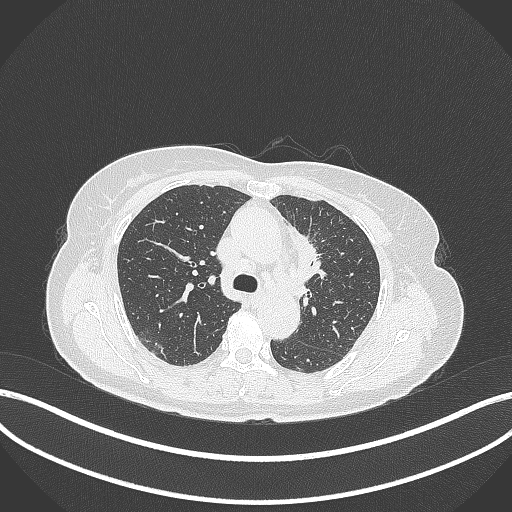
Chest CT, one axial slice. Slice 228 of 369 in the series (ordered by position). Reconstruction kernel B70f. Lung window (W 1500 / L -600 HU). 1 mm slice thickness. 512 × 512 image matrix. Female patient, age 65 years. Case-level facts recorded for this patient, not image findings: clinical TNM (as recorded): T2a N0 M0; histopathological grade: G2-3.
Outlined on this slice (bounding box drawn by a radiologist):
- lung tumour (recorded histology: adenocarcinoma): bounding box [x1, y1, x2, y2] px = [287, 224, 320, 282]